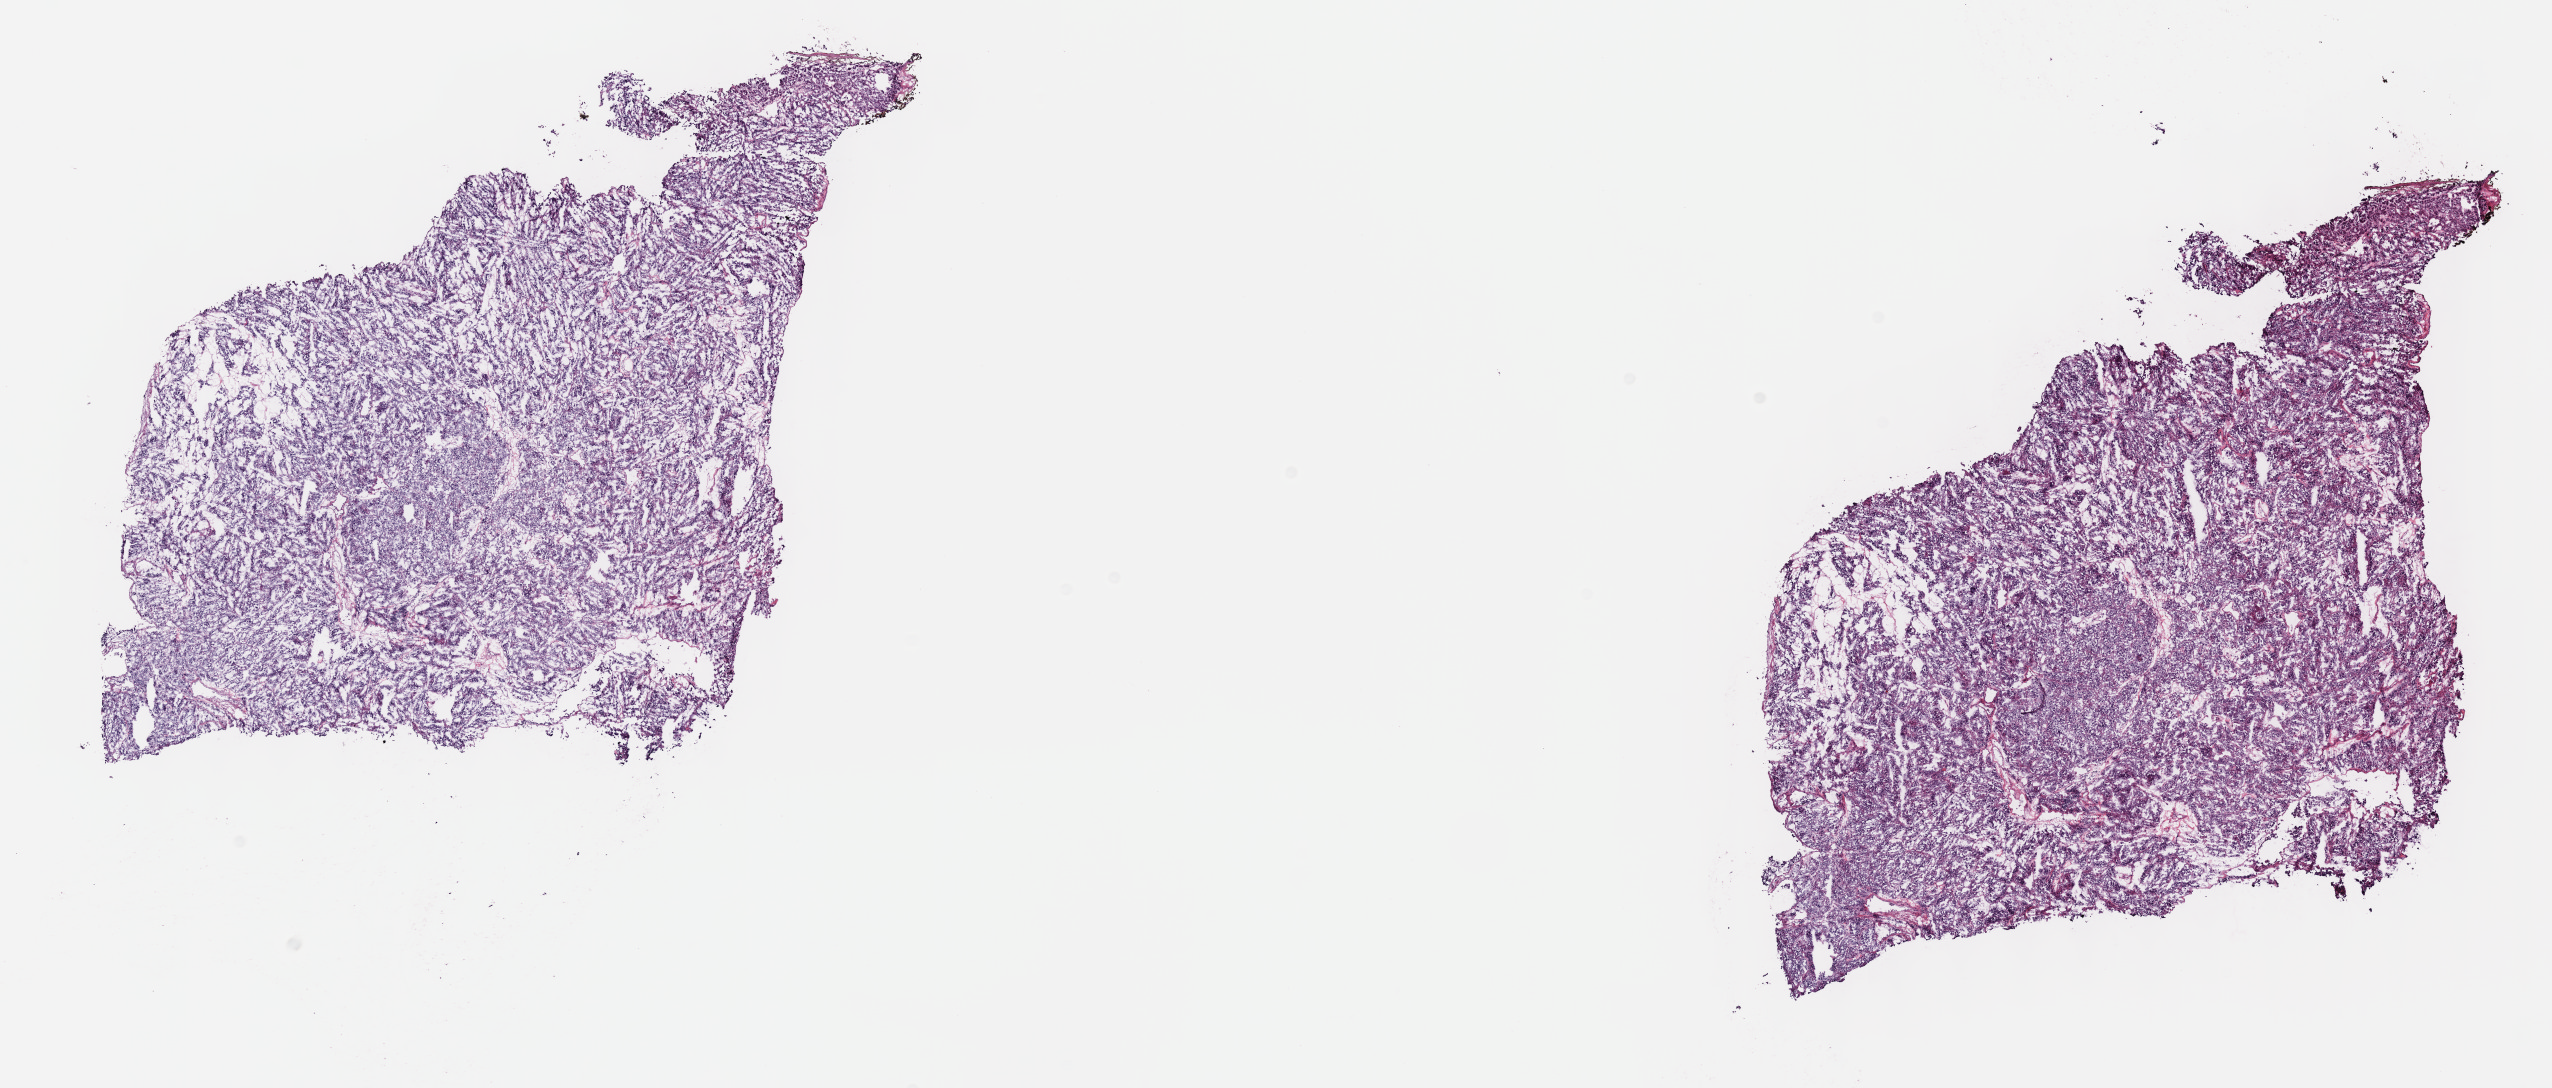
H&E whole-slide image — whole scanned area (about 20.6 x 8.8 mm, acquisition: 40x scan) shown as a low-resolution overview; frozen section from the top of the tissue portion; adrenal gland, primary tumour sample. Male, age 59 years at initial diagnosis.
Histologic diagnosis: Pheochromocytoma, NOS.